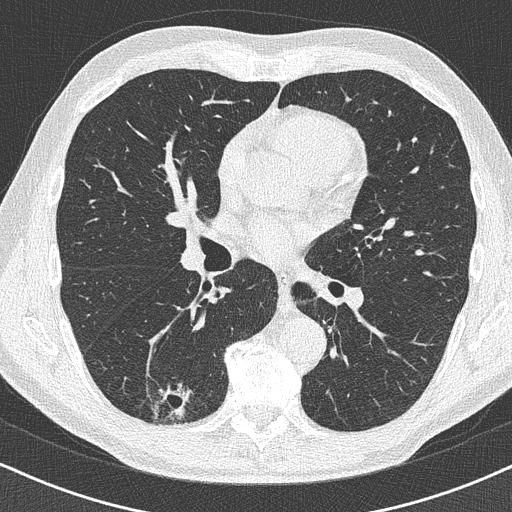
Low-dose screening chest CT, one axial slice; slice 230 of 438 in the series (ordered by position); reconstruction kernel B50f; 120 kVp; lung window (W 1500 / L -600 HU); 512 × 512 image matrix, field of view 320 × 320 mm.
Structures marked on this image (outlined manually by an expert reader):
- lesion 1 (tumor, lower lobe of right lung): box from (x=174, y=388) to (x=190, y=416) px